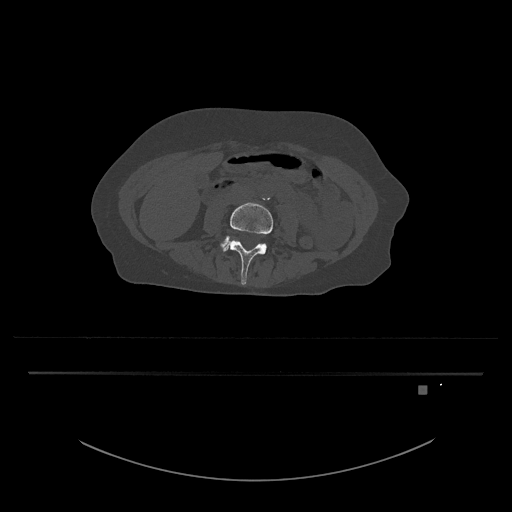
CT including the spine, one axial slice; slice 358 of 797 in the series (ordered by position); bone window (W 1800 / L 400 HU); 512 × 512 image matrix, field of view 500 × 500 mm. Patient: female, 57 years. Case-level facts recorded for this patient, not image findings: primary cancer: cervical.
Structures marked on this image (semi-automatic segmentation, software-assisted and operator-edited):
- L4 vertebra: bounding box <222,202,273,285> (left, top, right, bottom; pixels)